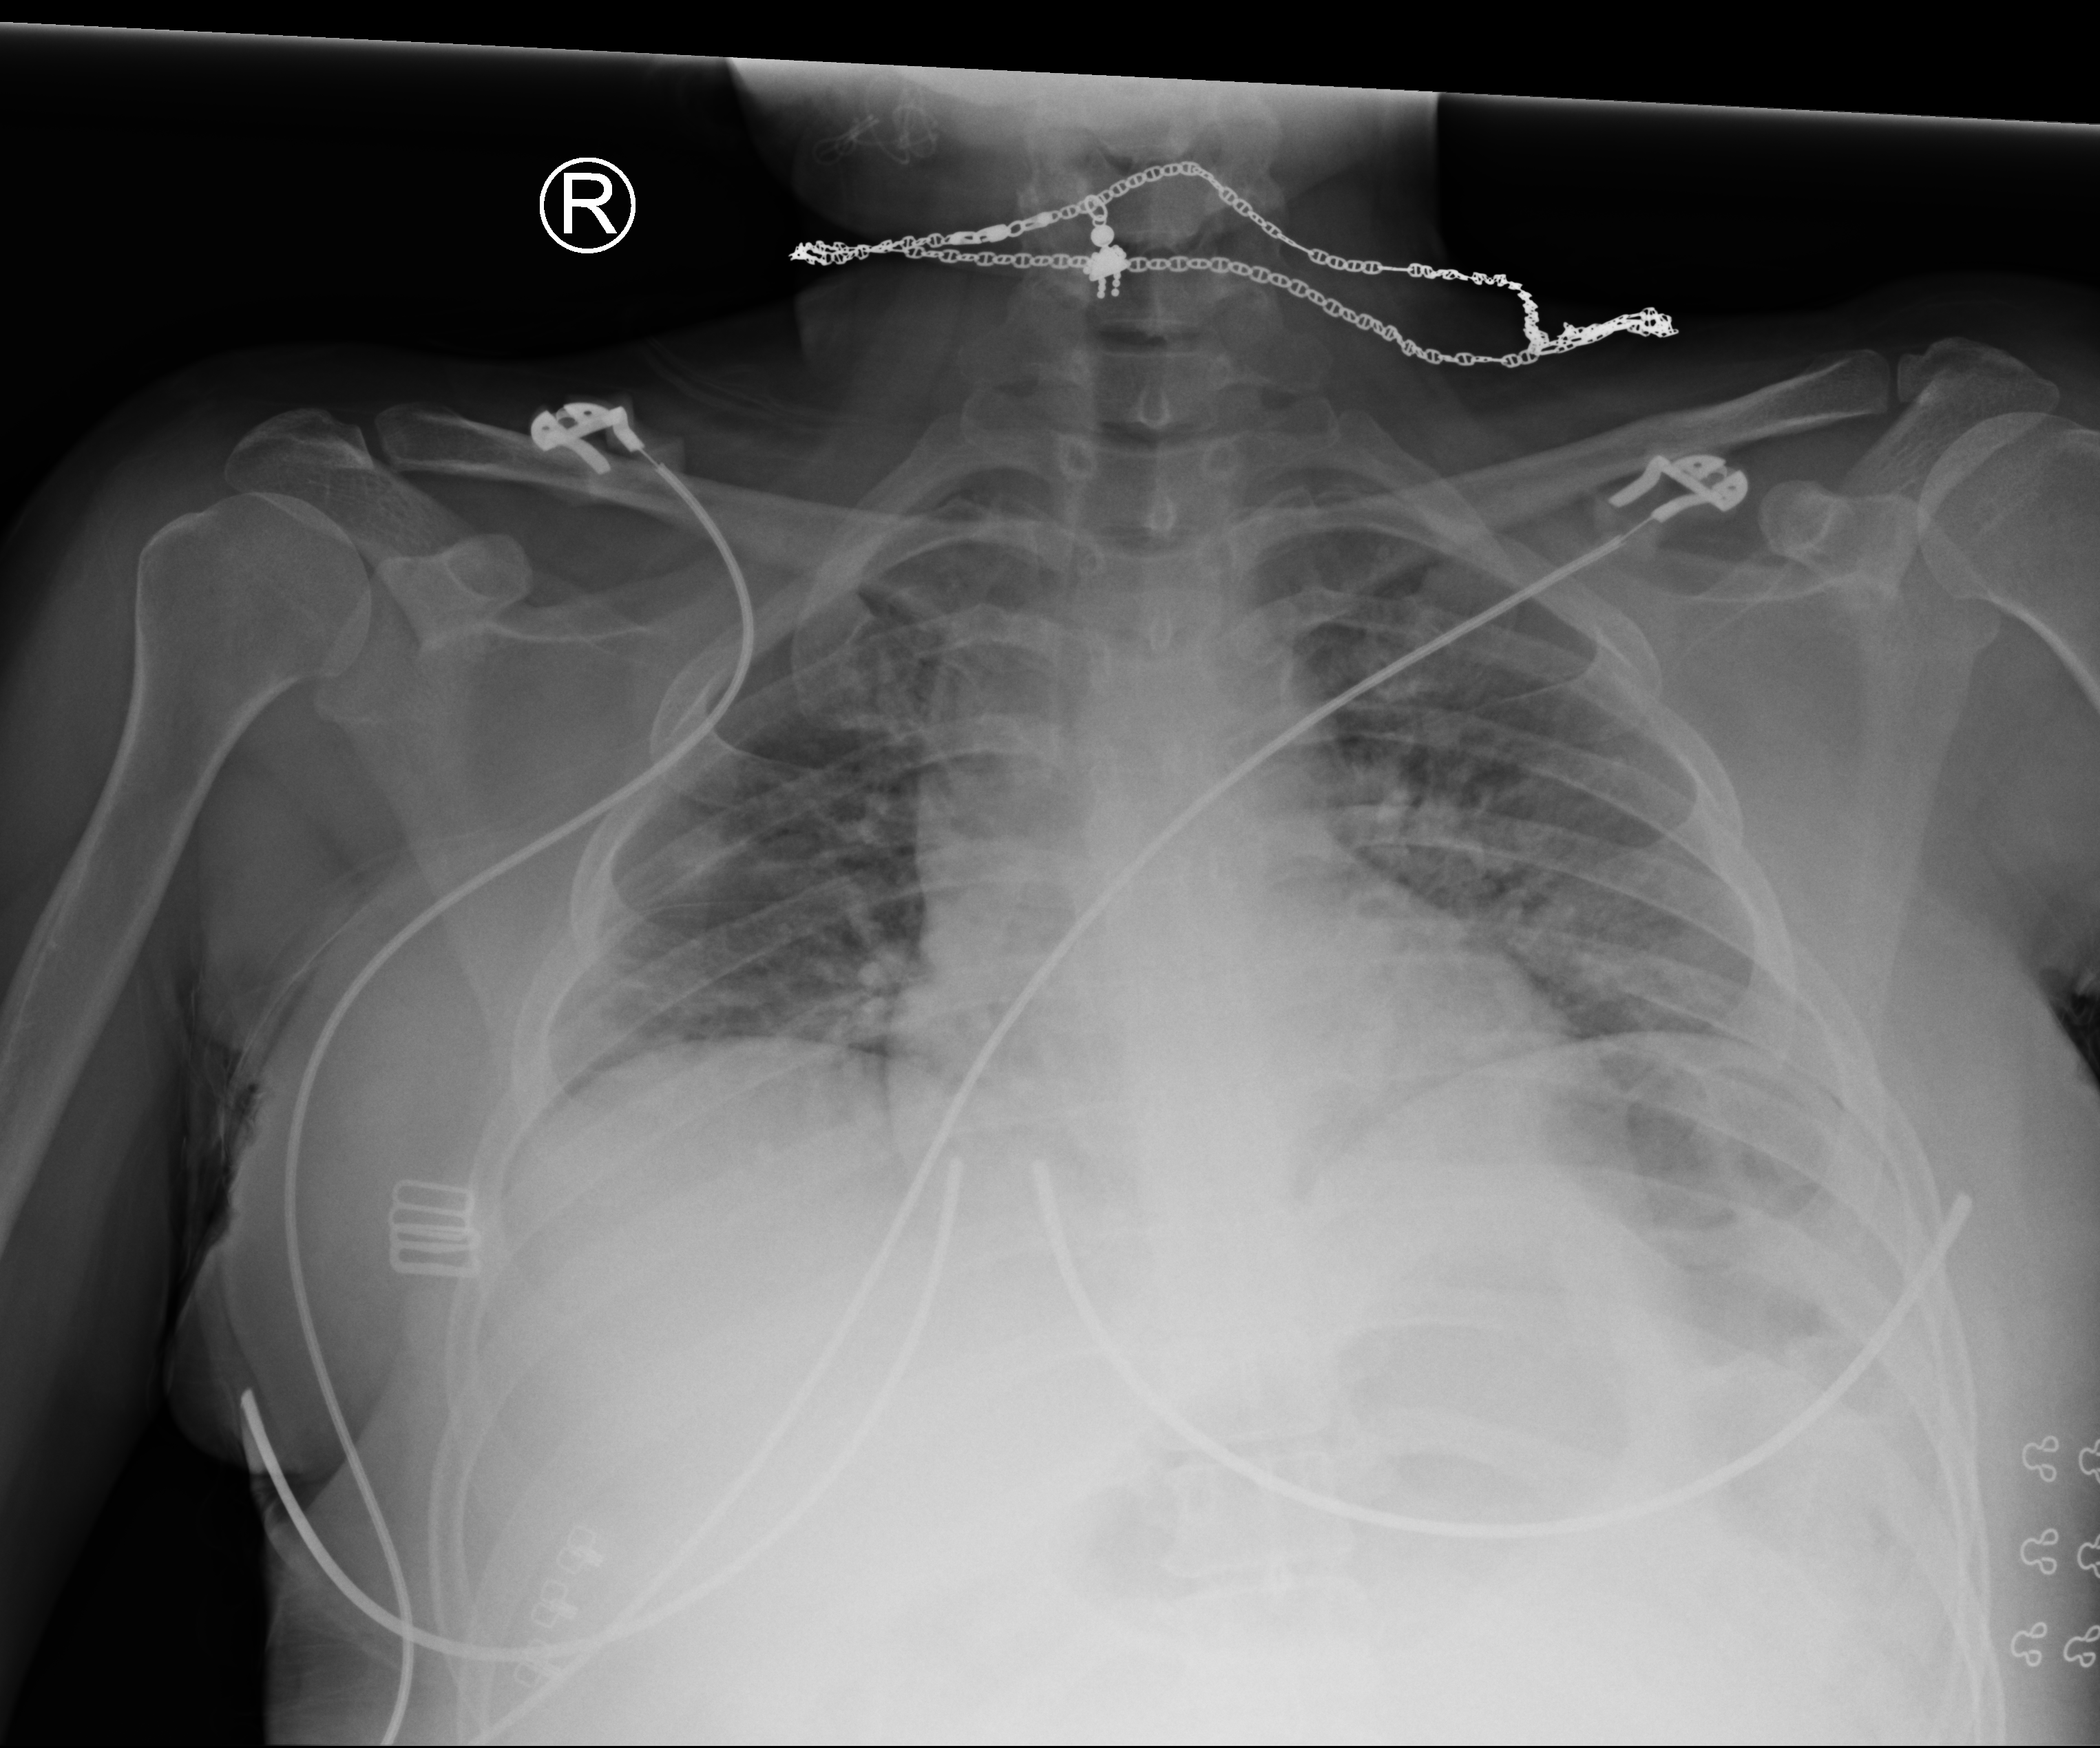
Chest X-ray (portable), anteroposterior (AP) projection. Female patient hospitalised with COVID-19, age 18–59 years.
Hospital-stay facts (about this admission, not read from this image; timing relative to this image not recorded):
- smoking status (admission record): never
- mechanically ventilated during this hospital stay: no